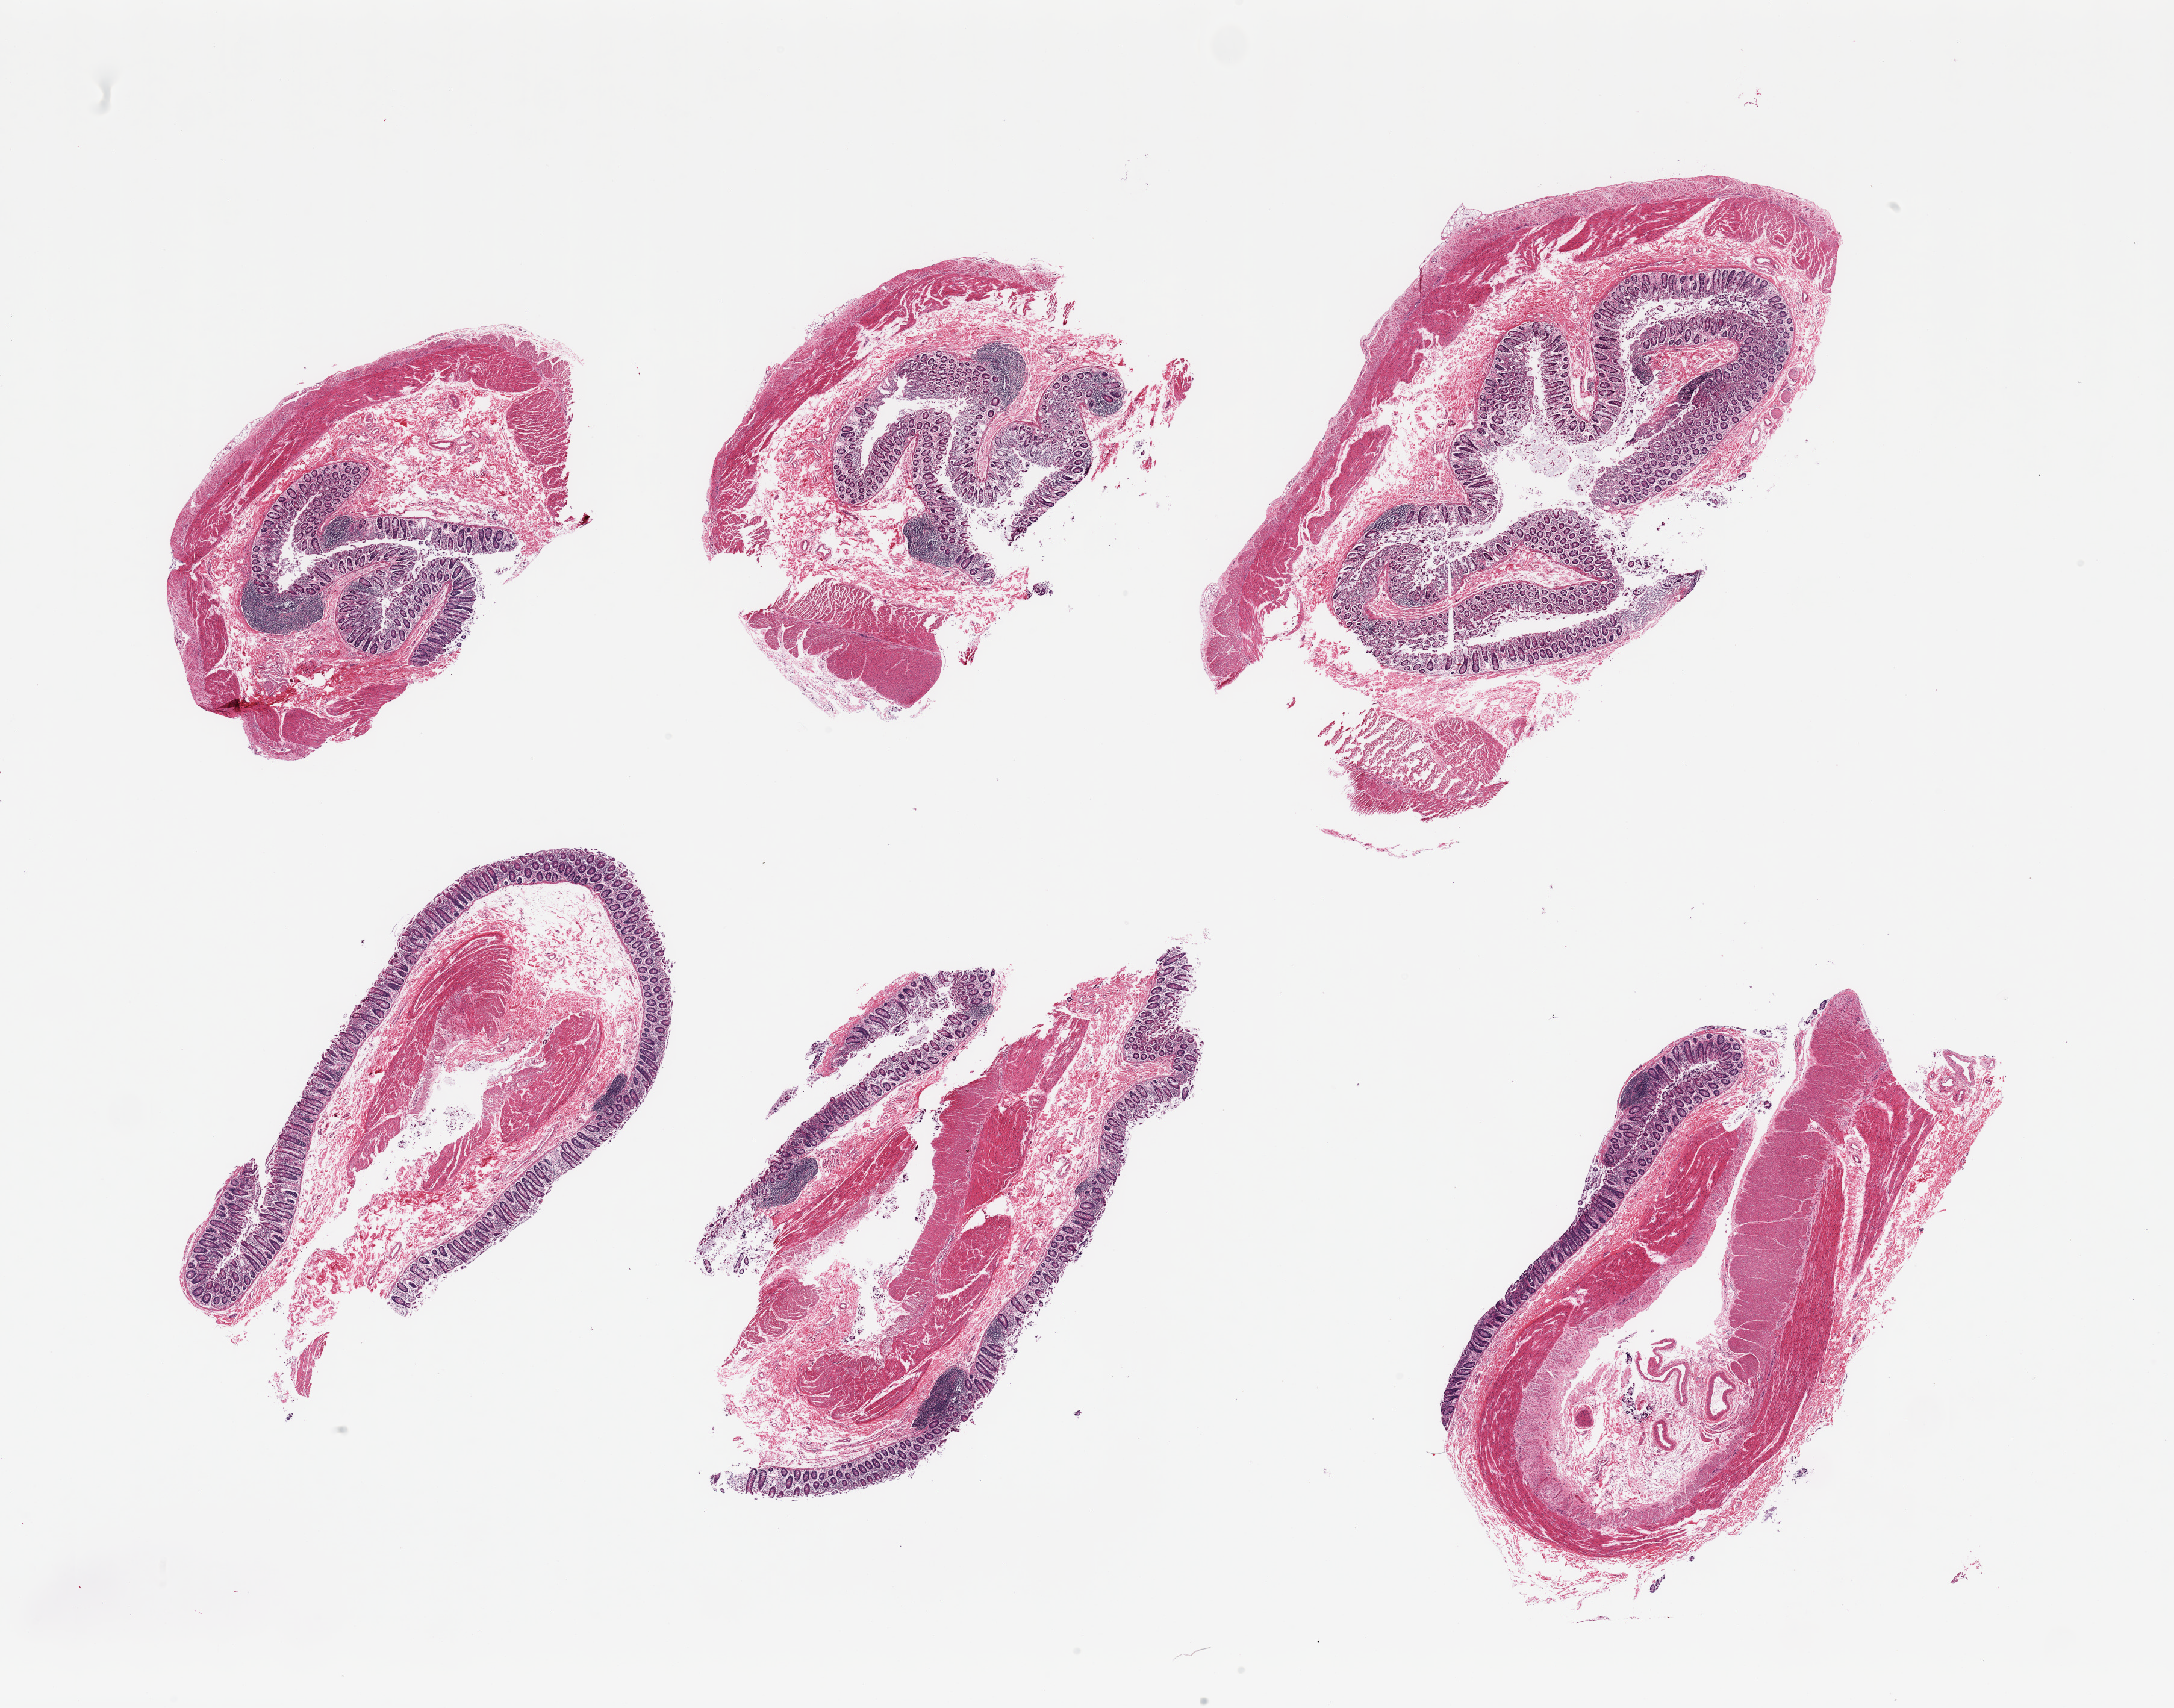
Whole-slide image, H&E stain, brightfield — a low-resolution overview of the entire scanned area, about 28.5 x 22.4 mm; PAXgene-fixed, paraffin-embedded tissue; target tissue: transverse colon; tissue donor sample. Donor: male.
Reviewer comment on this tissue sample: 6 pieces; moderately autolyzed mucosa and well preserved lymphoid aggregates and muscularis.